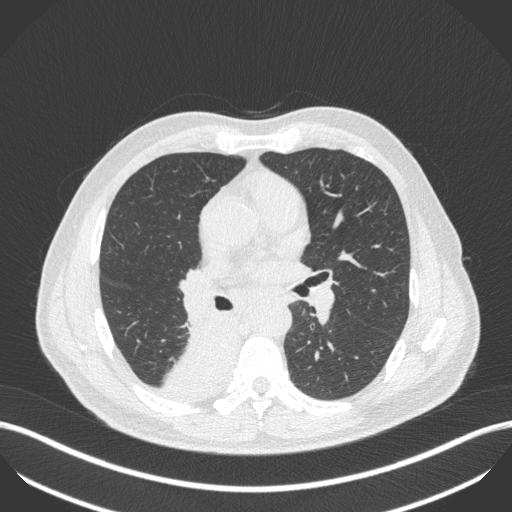
Chest CT, one axial slice. Slice 259 of 451 in the series (ordered by position). 100 kVp. Lung window (W 1500 / L -600 HU). 512 × 512 image matrix, field of view 400 × 400 mm. Male patient, age 61 years. Case-level facts recorded for this patient, not image findings: clinical TNM (as recorded): T1 N0 M0.
Annotated regions visible in this slice (rectangle marked by the reading radiologist):
- lung tumour (recorded histology: small cell carcinoma): box from (x=164, y=315) to (x=233, y=397) px